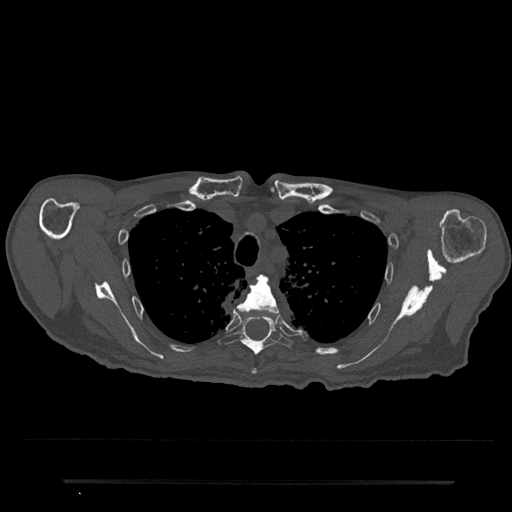
CT including the spine, one axial slice; position 594 of 797 along the scan axis; 120 kVp; bone window (W 1800 / L 400 HU); 0.5 mm slice thickness; 512 × 512 image matrix, field of view 427 × 427 mm. Male patient, age 74 years. From the clinical record (not read from this slice): primary cancer: prostate.
Annotated regions visible in this slice (semi-automatic segmentation, software-assisted and operator-edited):
- T4 vertebra: bounding box (x1, y1, x2, y2) in pixels: (237, 275, 280, 374)
- T5 vertebra: (218, 316, 294, 355)